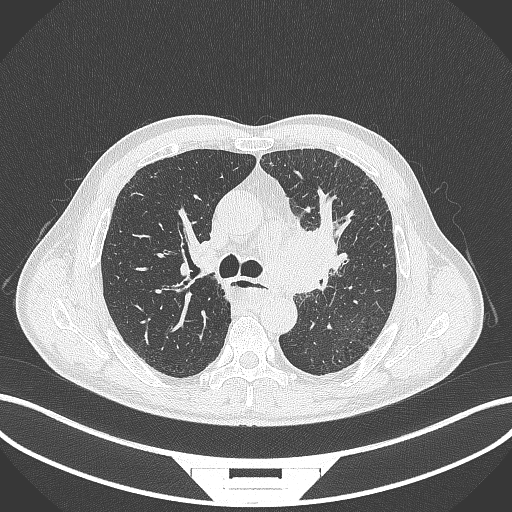
Chest CT, one axial slice. Slice 248 of 411 in the series (ordered by position). Lung window (W 1500 / L -600 HU). 1 mm slice thickness. 512 × 512 image matrix, field of view 400 × 400 mm. Patient: male, 57 years. Case-level facts recorded for this patient, not image findings: clinical TNM (as recorded): T2a N1 M0.
Structures marked on this image (bounding box drawn by a radiologist):
- lung tumour (recorded histology: squamous cell carcinoma): bounding box <280,214,347,302> (left, top, right, bottom; pixels)